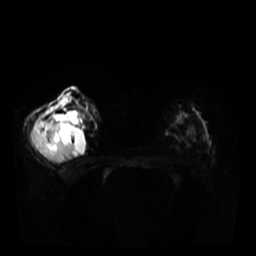
Breast MRI, one axial slice; position 21 of 34 along the scan axis; diffusion-weighted series; image 2 of 4 stored at this slice position (different b-values; order by instance number); 3 T; 5 mm slice thickness; 256 × 256 image matrix, field of view 320 × 320 mm. Female patient.
Outlined on this slice (expert manual segmentation):
- tumour on diffusion-weighted imaging: bounding box (x1, y1, x2, y2) in pixels: (34, 120, 77, 162)